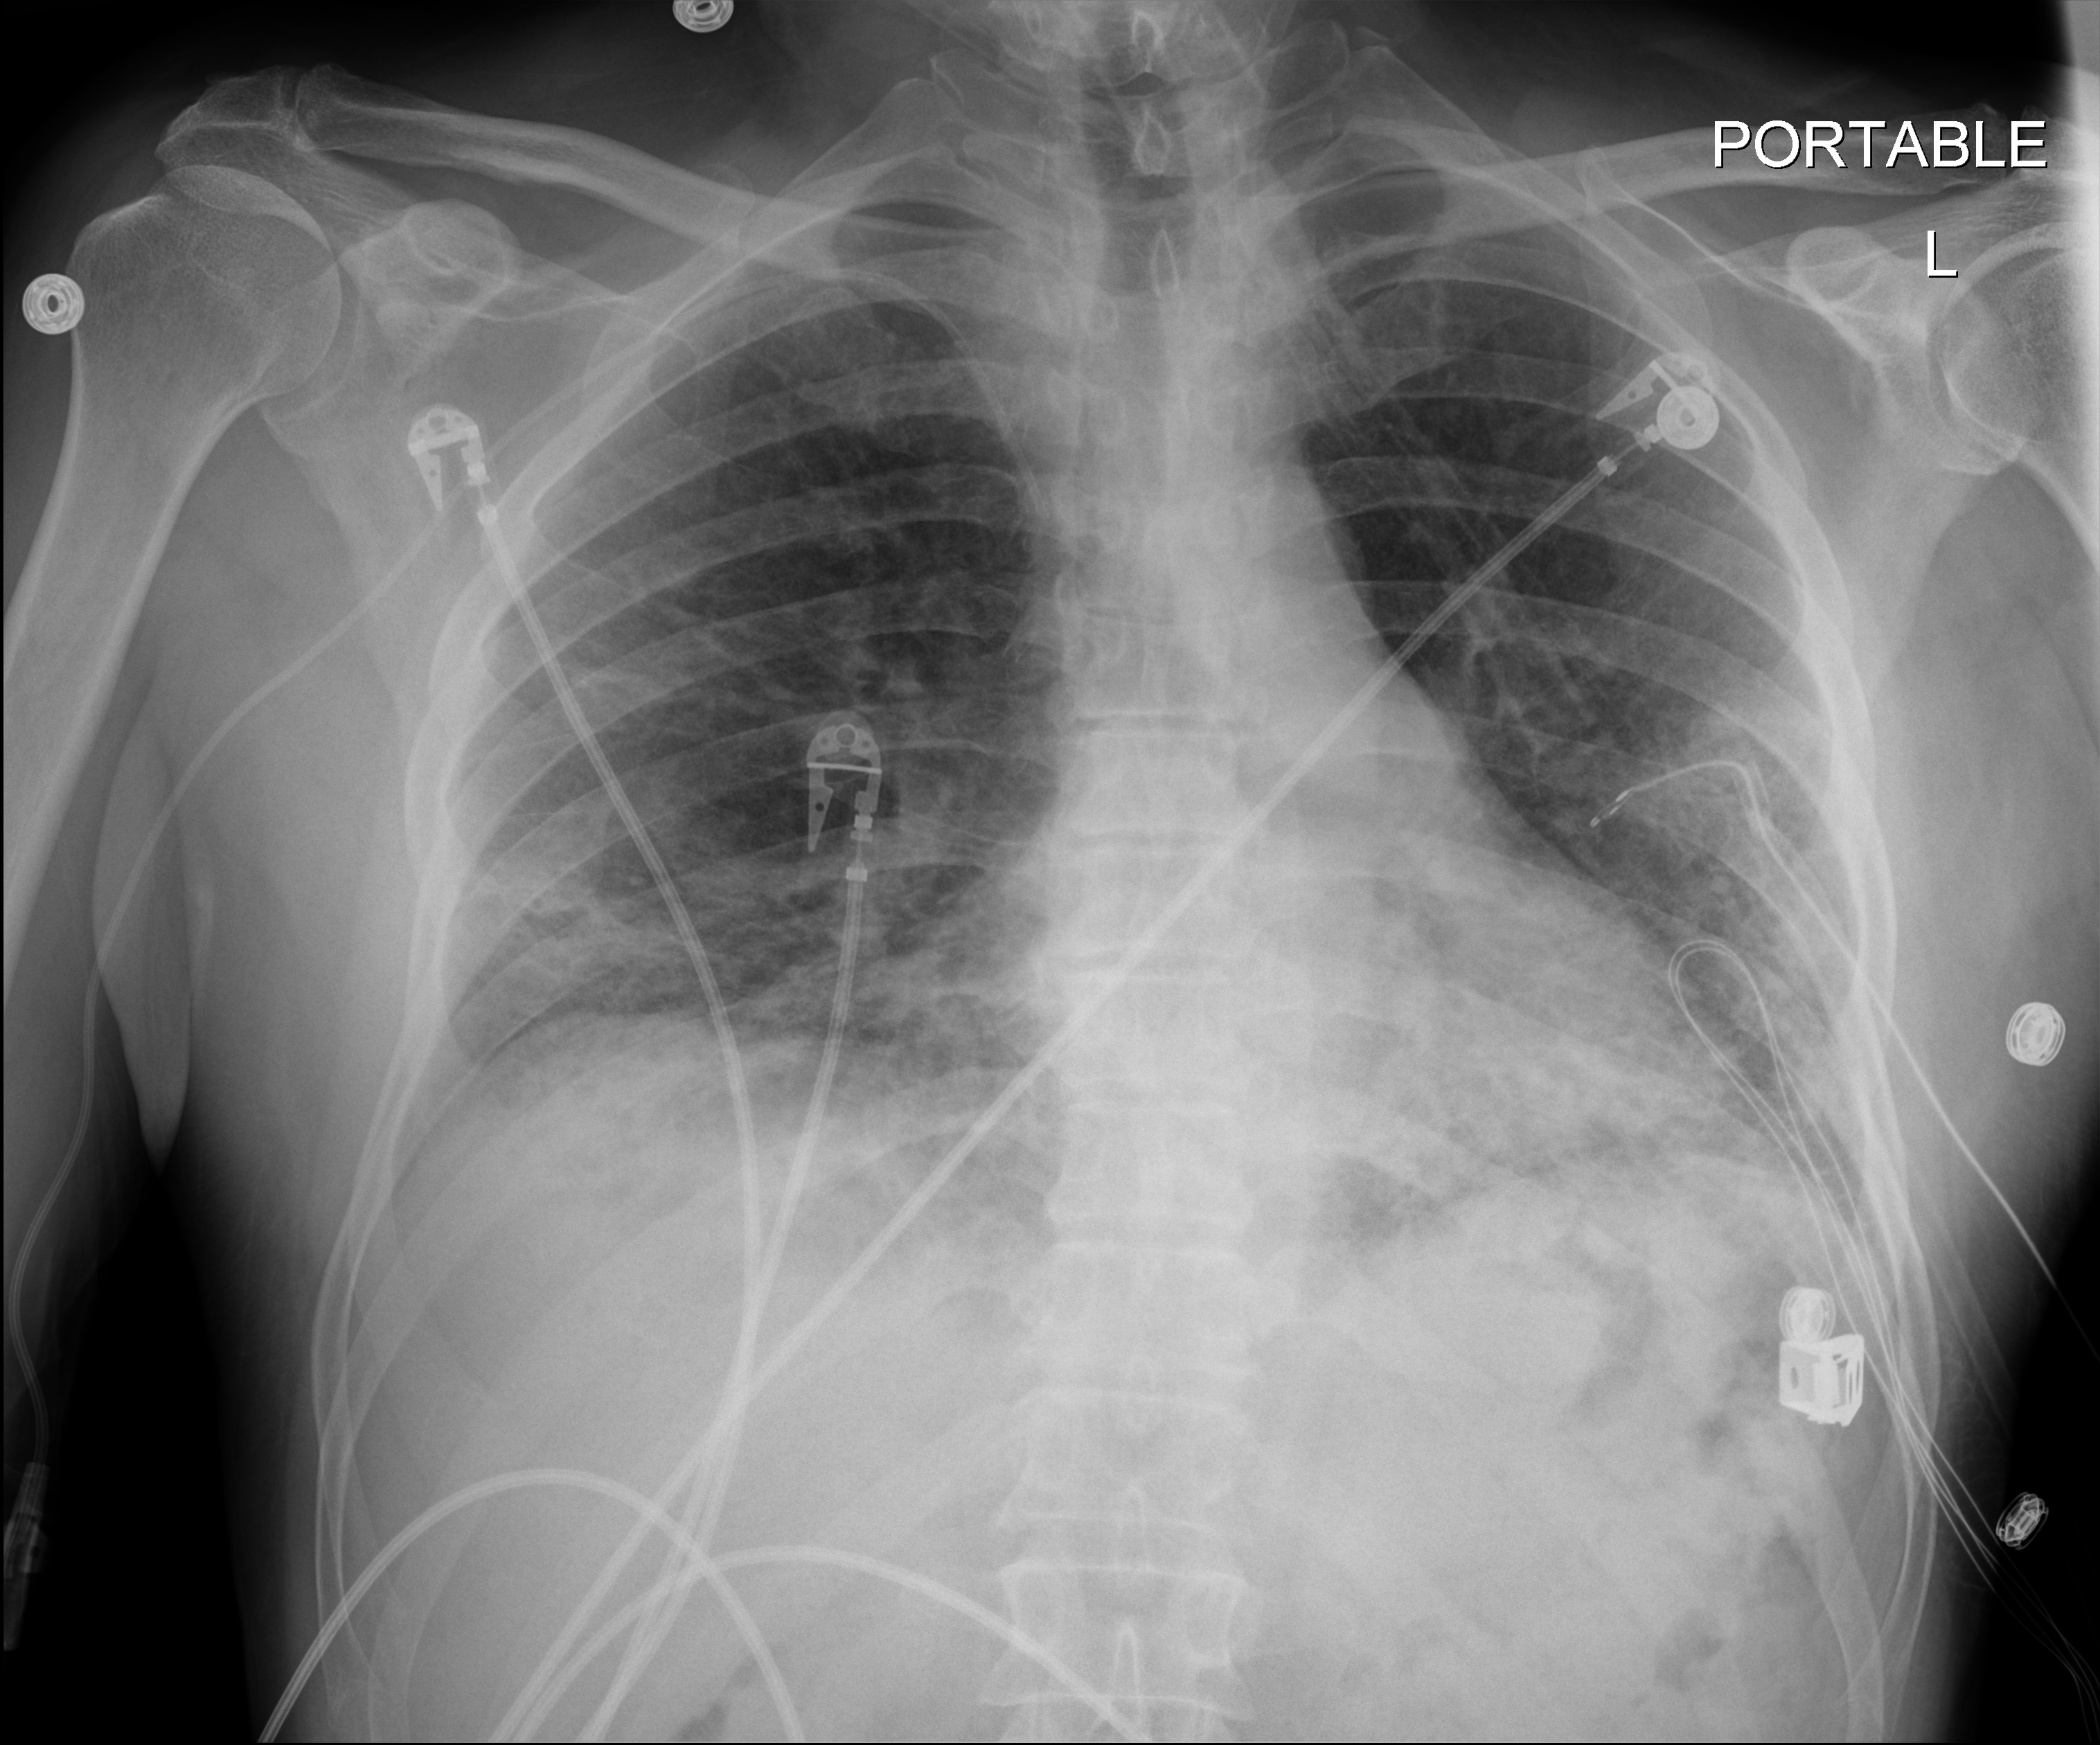
Chest X-ray (portable), anteroposterior (AP) projection. Male patient hospitalised with COVID-19, age 18–59 years.
From the hospital-stay record, not from the radiograph (when in the stay this image was taken is not recorded):
- length of hospital stay: 38 days